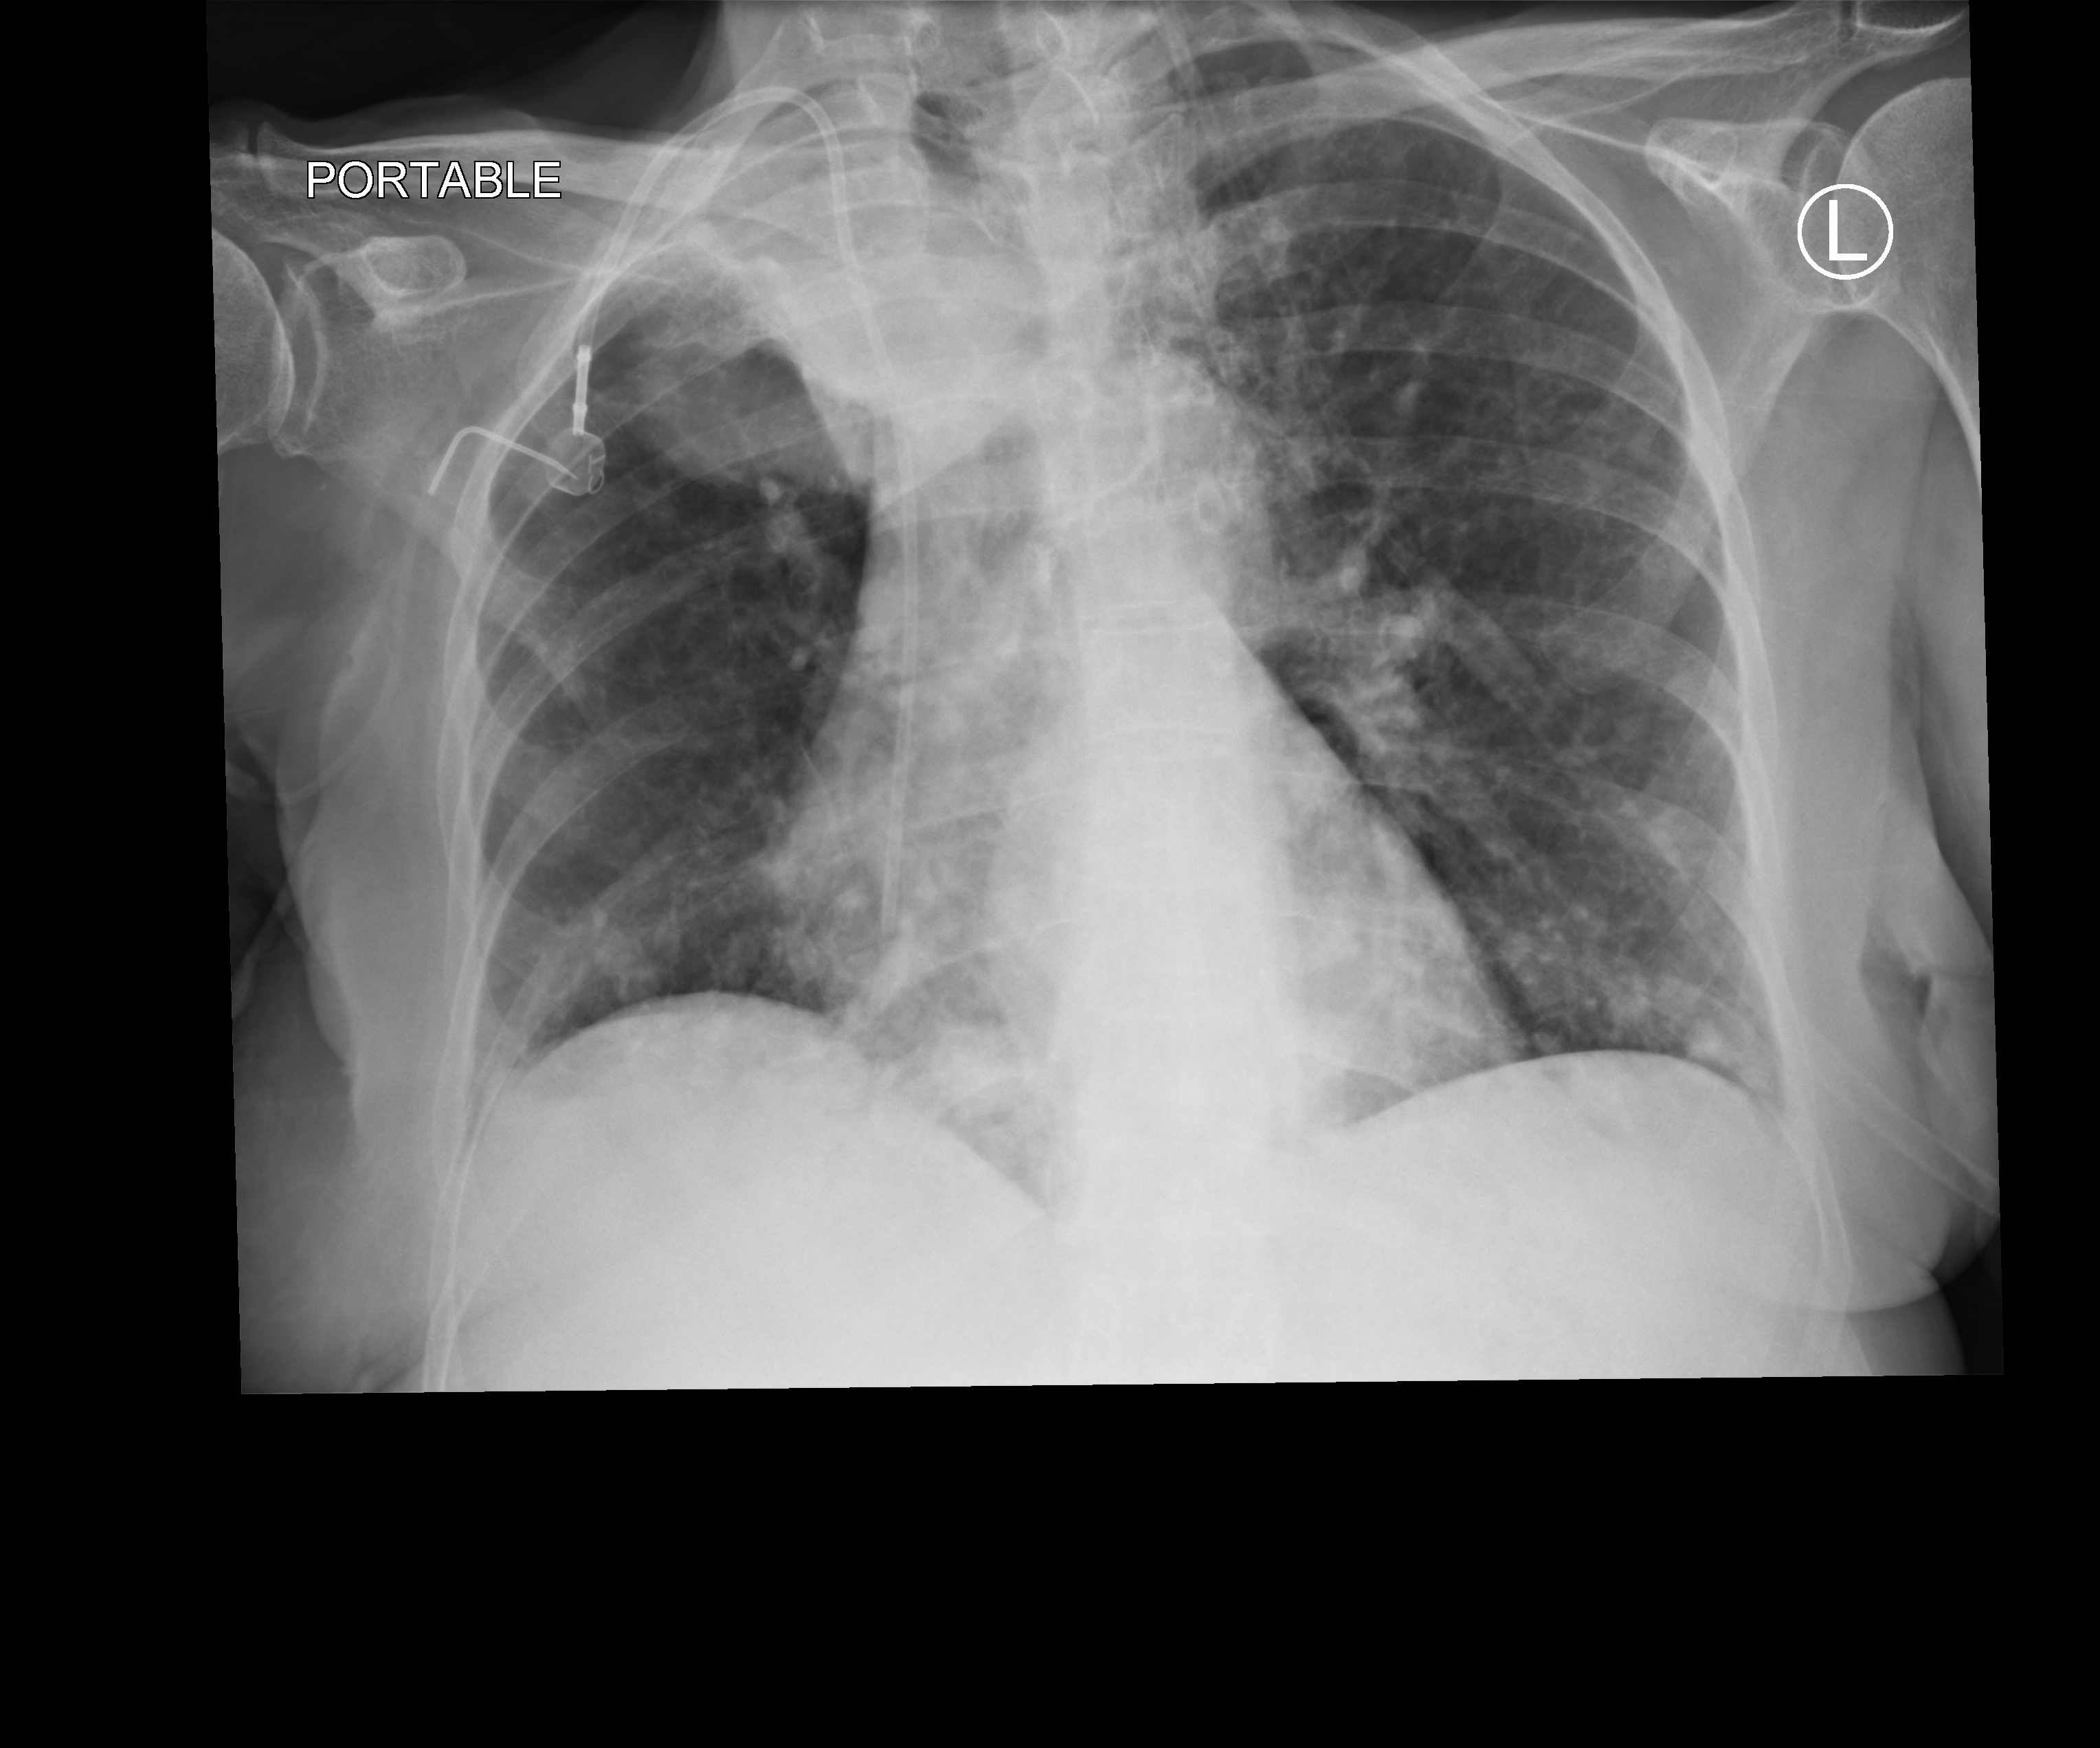
Bedside chest radiograph (computed radiography); anteroposterior (AP) projection. Female patient hospitalised with COVID-19, age 60–74 years.
Admission-level facts for this patient (not findings on this image; timing relative to this image not recorded):
- admitted to intensive care during this hospital stay: no
- length of hospital stay: 8 days